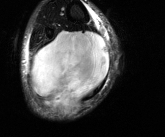
MRI of an extremity soft-tissue mass, one axial slice. Slice 42 of 81 in the series (ordered by position). T2-weighted fat-saturated. MR volume resampled by the dataset authors to the PET/CT grid (not the native acquisition matrix). 165 × 137 image matrix, field of view 161 × 134 mm. Male patient. Case-level facts recorded for this patient, not image findings: histological type: liposarcoma - round cell; grade: high; site of the primary tumour: right calf.
Outlined on this slice (expert contour drawn on MRI and transferred to this co-registered scan by the dataset authors):
- gross tumour volume (mass): bounding box [x1, y1, x2, y2] px = [30, 30, 109, 115]